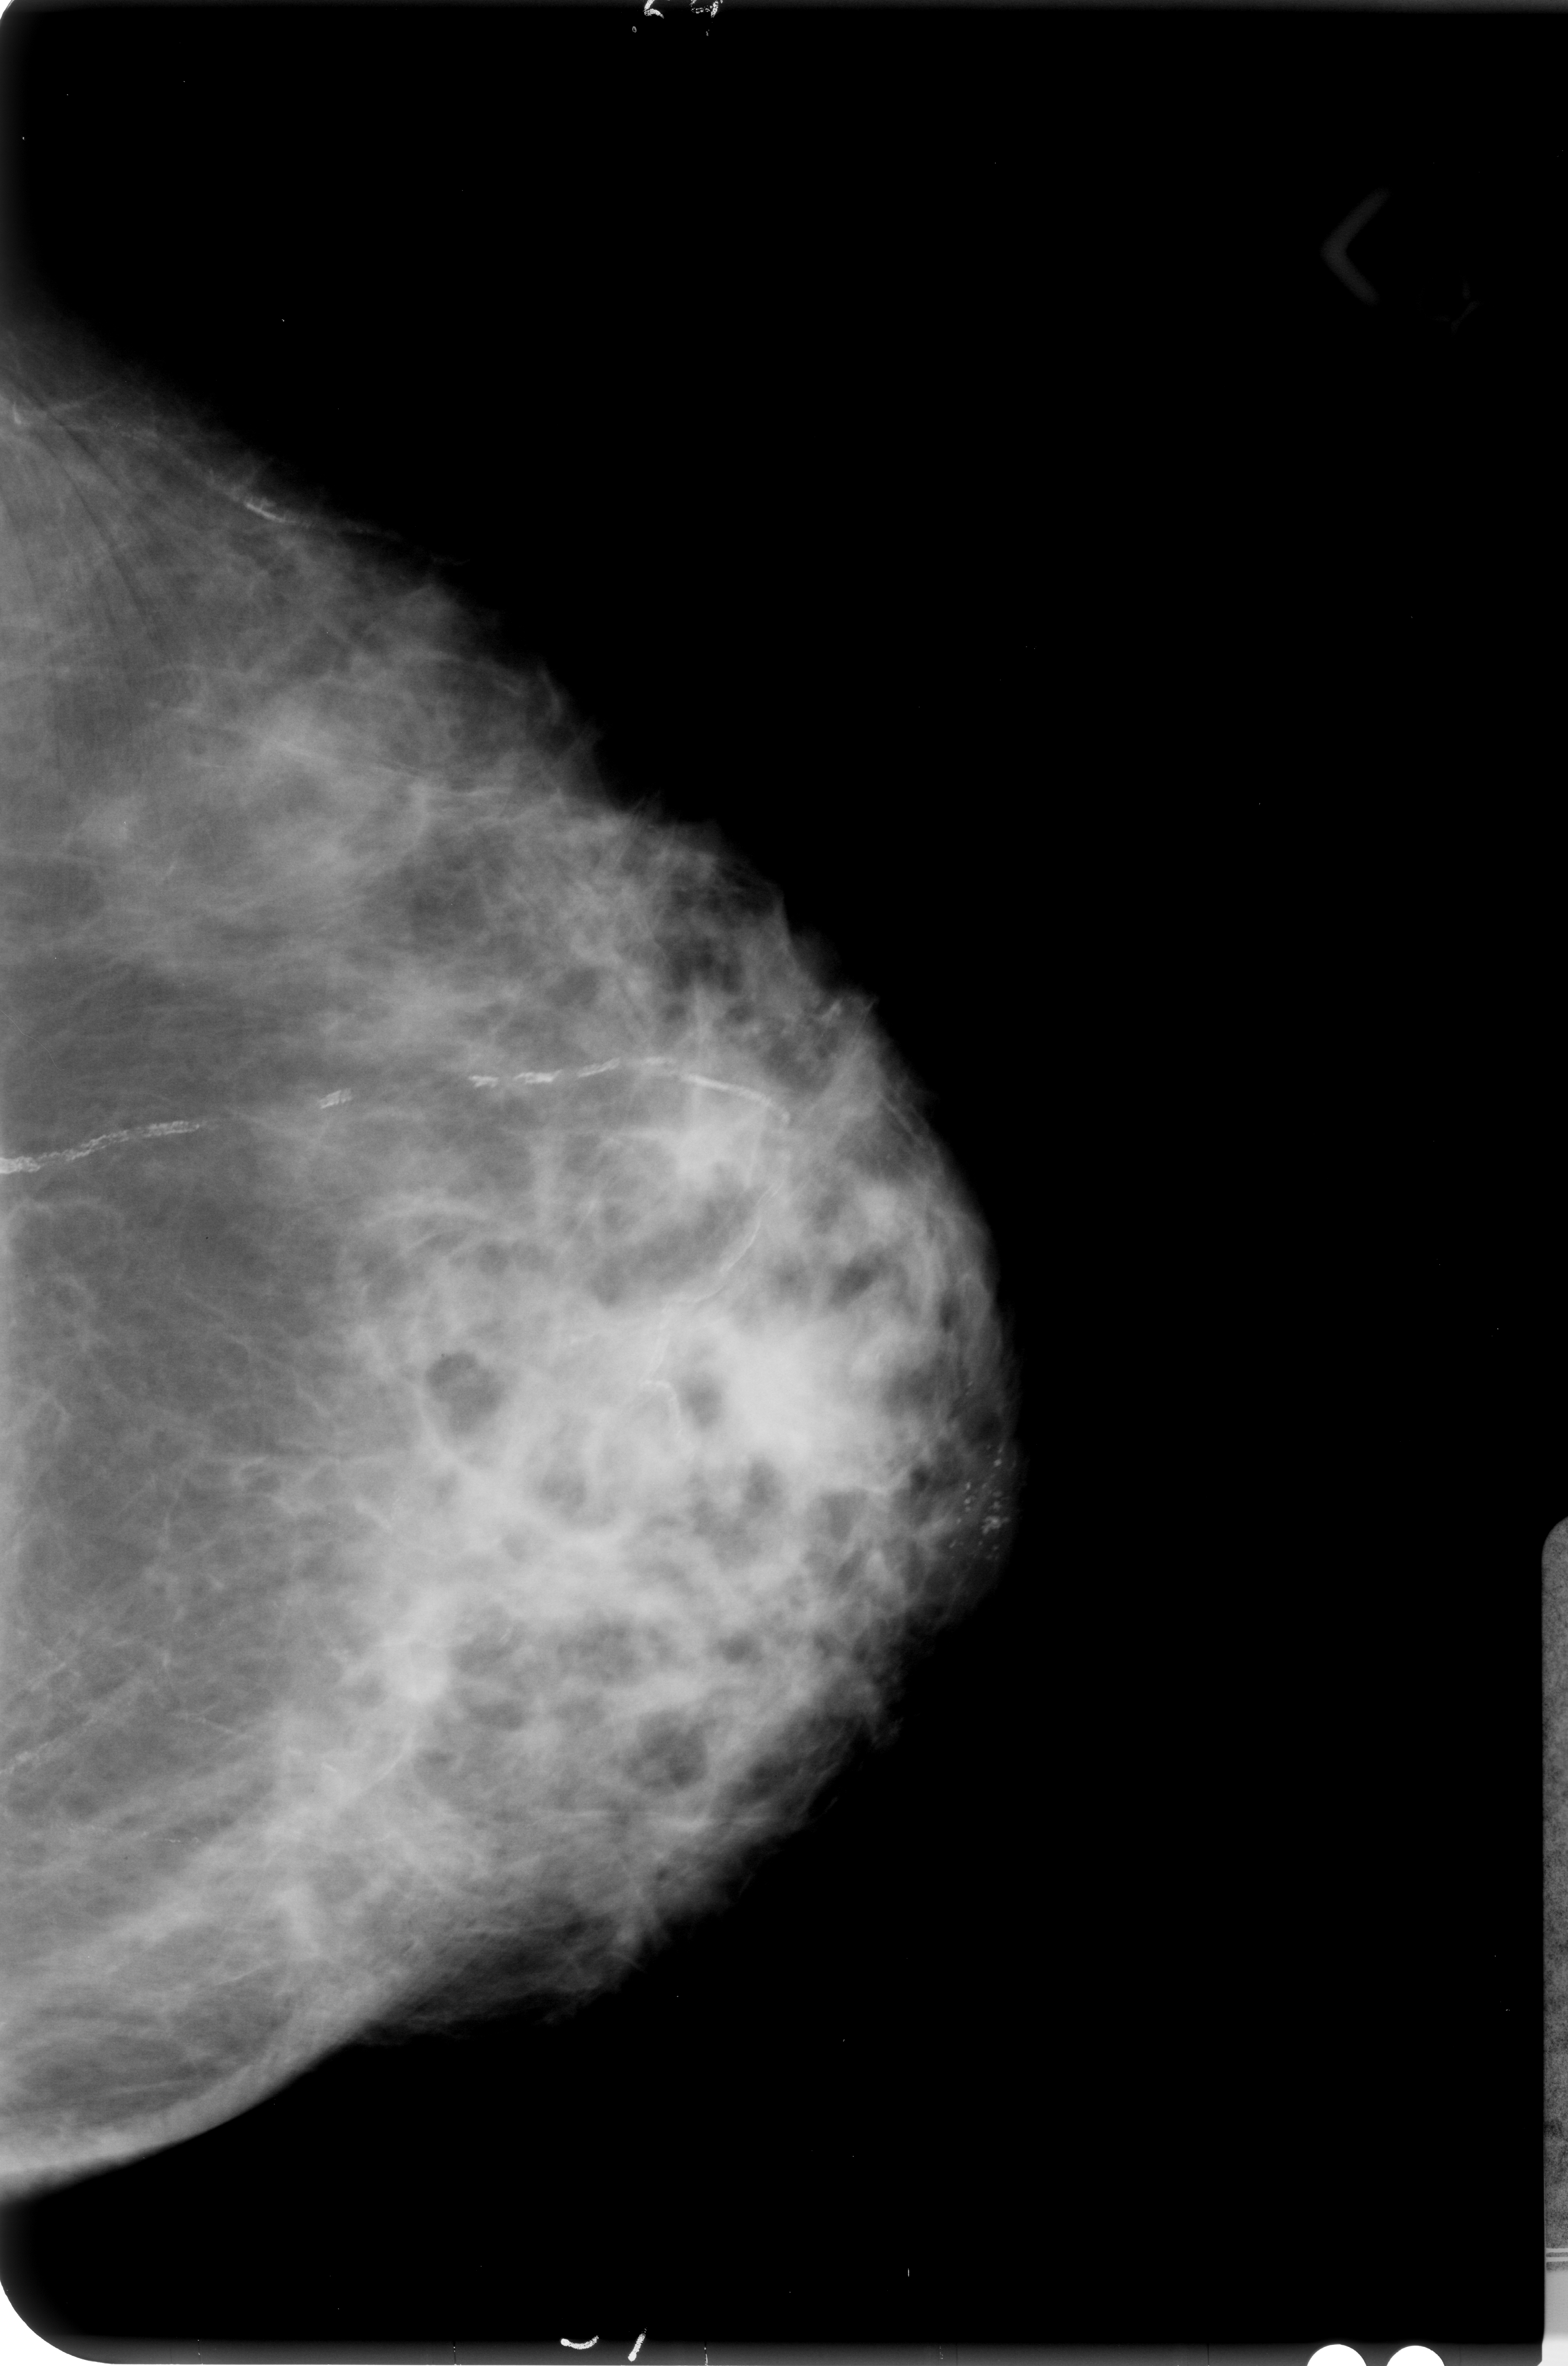
Scanned film-screen mammogram; left breast; craniocaudal (CC) view; BI-RADS breast density category 2 (scale 1–4); 1568 × 2366 image matrix.
Expert-marked regions of interest on this film, with their recorded descriptors:
- calcifications, morphology pleomorphic, distribution clustered; BI-RADS assessment category 4; subtlety rating 4 on a 1 (subtle) to 5 (obvious) scale; pathology (as recorded): malignant: bounding box [x1, y1, x2, y2] px = [930, 1439, 1044, 1633]